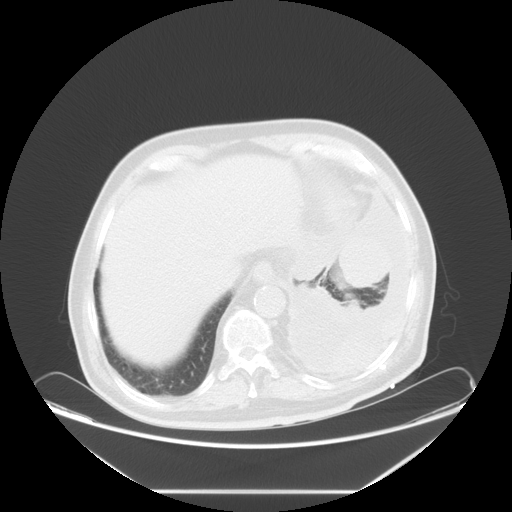
Chest CT, one axial slice; position 15 of 63 along the scan axis; lung window (W 1500 / L -600 HU); 5 mm slice thickness; 512 × 512 image matrix. Patient: male, 67 years. Case-level facts recorded for this patient, not image findings: clinical TNM (as recorded): T1b N1 M1a; histopathological grade: G3.
Outlined on this slice (rectangle marked by the reading radiologist):
- lung tumour (recorded histology: small cell carcinoma): bounding box <339,232,394,290> (left, top, right, bottom; pixels)